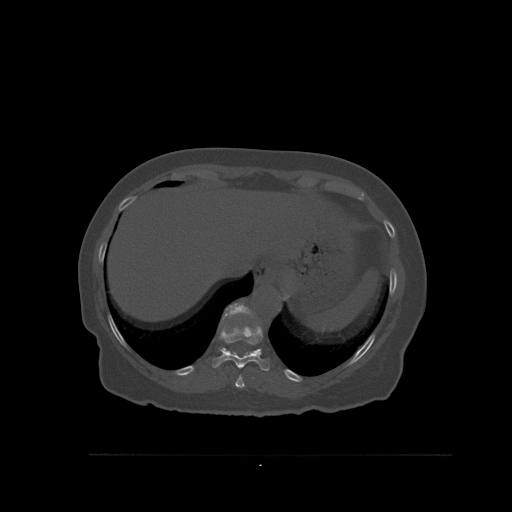
CT including the spine, one axial slice. Position 318 of 527 along the scan axis. Bone window (W 1800 / L 400 HU). 1.5 mm slice thickness. 512 × 512 image matrix, field of view 470 × 470 mm. Female patient, age 73 years. Case-level facts recorded for this patient, not image findings: primary cancer: breast.
Structures marked on this image (semi-automatic segmentation, software-assisted and operator-edited):
- T10 vertebra: bounding box (x1, y1, x2, y2) in pixels: (212, 325, 270, 371)
- T11 vertebra: (220, 303, 261, 350)
- T9 vertebra: (235, 375, 245, 389)